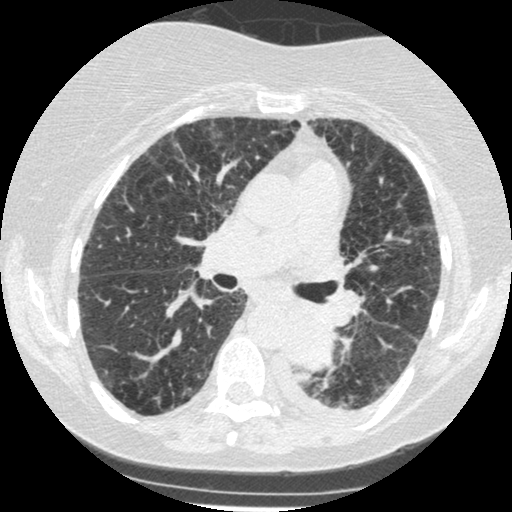
Low-dose screening chest CT, one axial slice; slice 145 of 341 in the series (ordered by position); 120 kVp; lung window (W 1500 / L -600 HU); 1.25 mm slice thickness; 512 × 512 image matrix.
Outlined on this slice (expert manual segmentation):
- lesion 1 (tumor, lower lobe of left lung): bounding box [x1, y1, x2, y2] px = [285, 307, 336, 369]